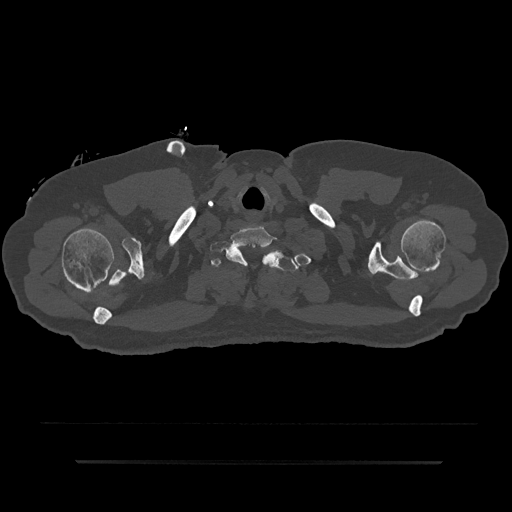
CT including the spine, one axial slice; slice 759 of 797 in the series (ordered by position); reconstruction kernel Br40s/3; 120 kVp; bone window (W 1800 / L 400 HU); 512 × 512 image matrix. Male patient, age 59 years. From the clinical record (not read from this slice): primary cancer: bile ducts; vertebrae with lytic lesions (as recorded): T10.
Outlined on this slice (semi-automatically segmented with operator editing):
- T1 vertebra: bounding box (x1, y1, x2, y2) in pixels: (211, 252, 300, 271)